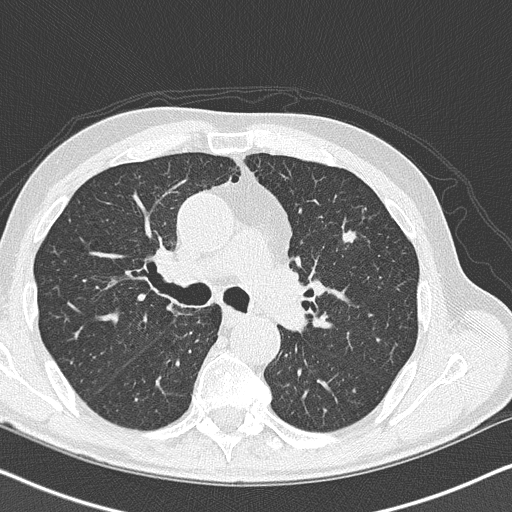
Low-dose screening chest CT, axial slice; second screening round (one year after baseline); lung window (W 1500 / L -600 HU); 2 mm slice thickness; 512 × 512 image matrix, field of view 330 × 330 mm. Male participant, aged 73 years at enrolment. Current smoker at enrolment.
Expert reader's lesion annotation, bounding box <316,219,376,270> (left, top, right, bottom; pixels). The screening reader recorded 3 non-calcified nodules or masses ≥4 mm on this exam (left upper lobe, left upper lobe, right lower lobe); which of them this box marks is not recorded. Official screen result: positive, other. Participant outcome: lung cancer diagnosed 36 days after this screen — small cell carcinoma, NOS, left upper lobe, stage IIIB (AJCC 6th edition), 19 mm at pathology.